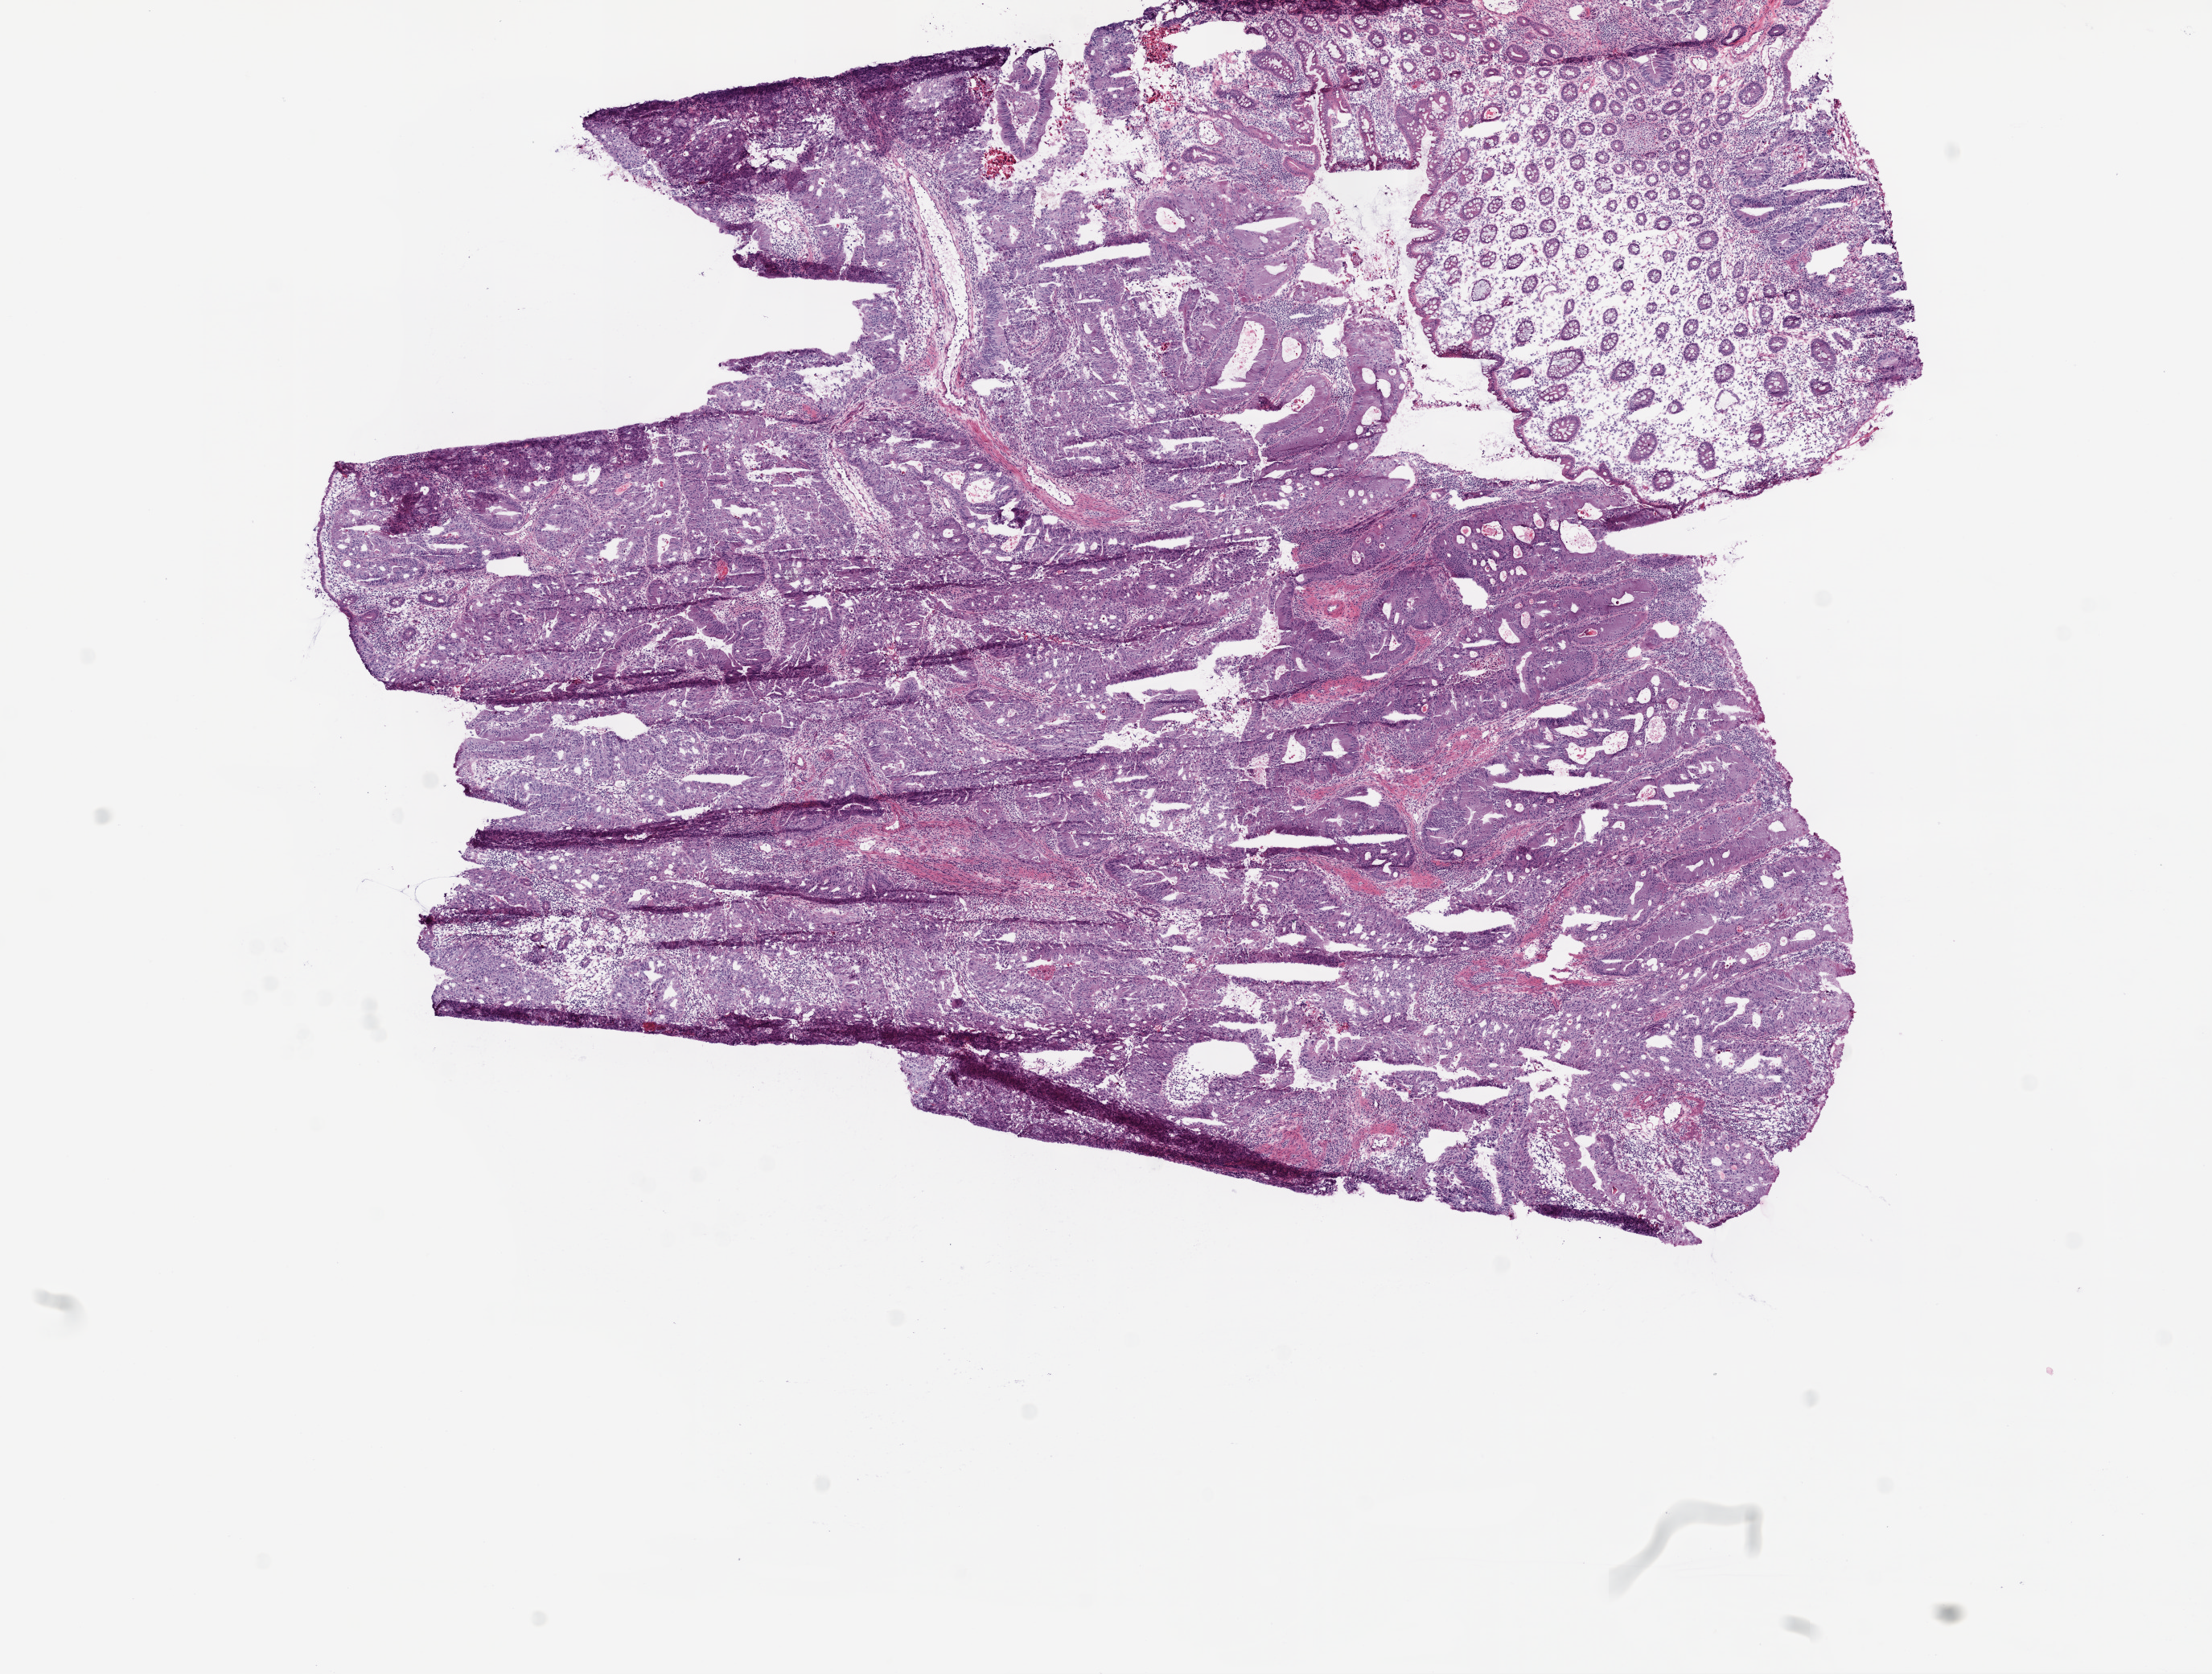
Whole-slide histology image, H&E — a low-resolution overview of the entire scanned area, about 11.0 x 8.3 mm (acquisition: 20x scan), frozen section from the top of the tissue portion, sample: primary tumour, colon. Male, age 85 years at initial diagnosis. Composition of this section per pathologist review: tumour cells 90%, tumour nuclei 90%, normal cells 5%, stromal cells 5%, necrosis 0%.
Diagnosis: Adenocarcinoma, NOS (cecum). TNM: T3 N2 M0. Lymph nodes positive (case pathology): 10 of 20 examined. AJCC pathologic stage: IIIC (6th edition).